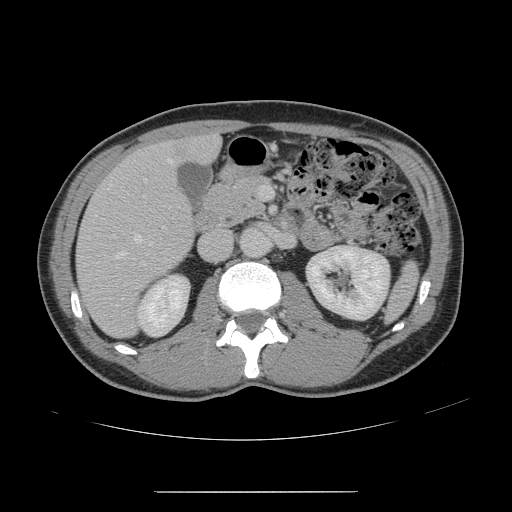
Contrast-enhanced abdominal CT, one axial slice; position 71 of 178 along the scan axis; intravenous contrast given; soft-tissue window (W 400 / L 40 HU); 2.5 mm slice thickness; 512 × 512 image matrix. Male patient, age 53 years. From the clinical record (not read from this slice): diagnosis: colorectal cancer liver metastases, imaged before liver resection.
Structures marked on this image (outlined manually by an expert reader):
- hepatic veins: bounding box <96,160,171,308> (left, top, right, bottom; pixels)
- liver: <77,137,220,337>
- planned liver remnant (the part of the liver to remain after resection): <192,137,220,160>
- portal vein (with intrahepatic branches): <144,186,267,198>